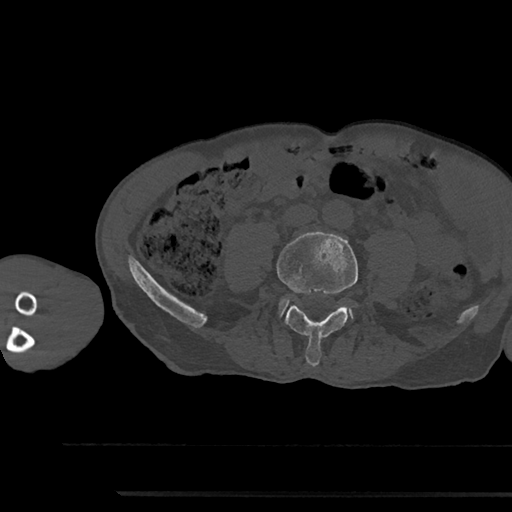
CT including the spine, one axial slice. Position 397 of 797 along the scan axis. Reconstruction kernel Br40s/3. 120 kVp. Bone window (W 1800 / L 400 HU). 0.5 mm slice thickness. 512 × 512 image matrix, field of view 367 × 367 mm. Patient: male, 79 years. Case-level facts recorded for this patient, not image findings: primary cancer: prostate.
Structures marked on this image (semi-automatic segmentation, software-assisted and operator-edited):
- L4 vertebra: bounding box (x1, y1, x2, y2) in pixels: (277, 232, 358, 367)
- L5 vertebra: (280, 299, 288, 316)